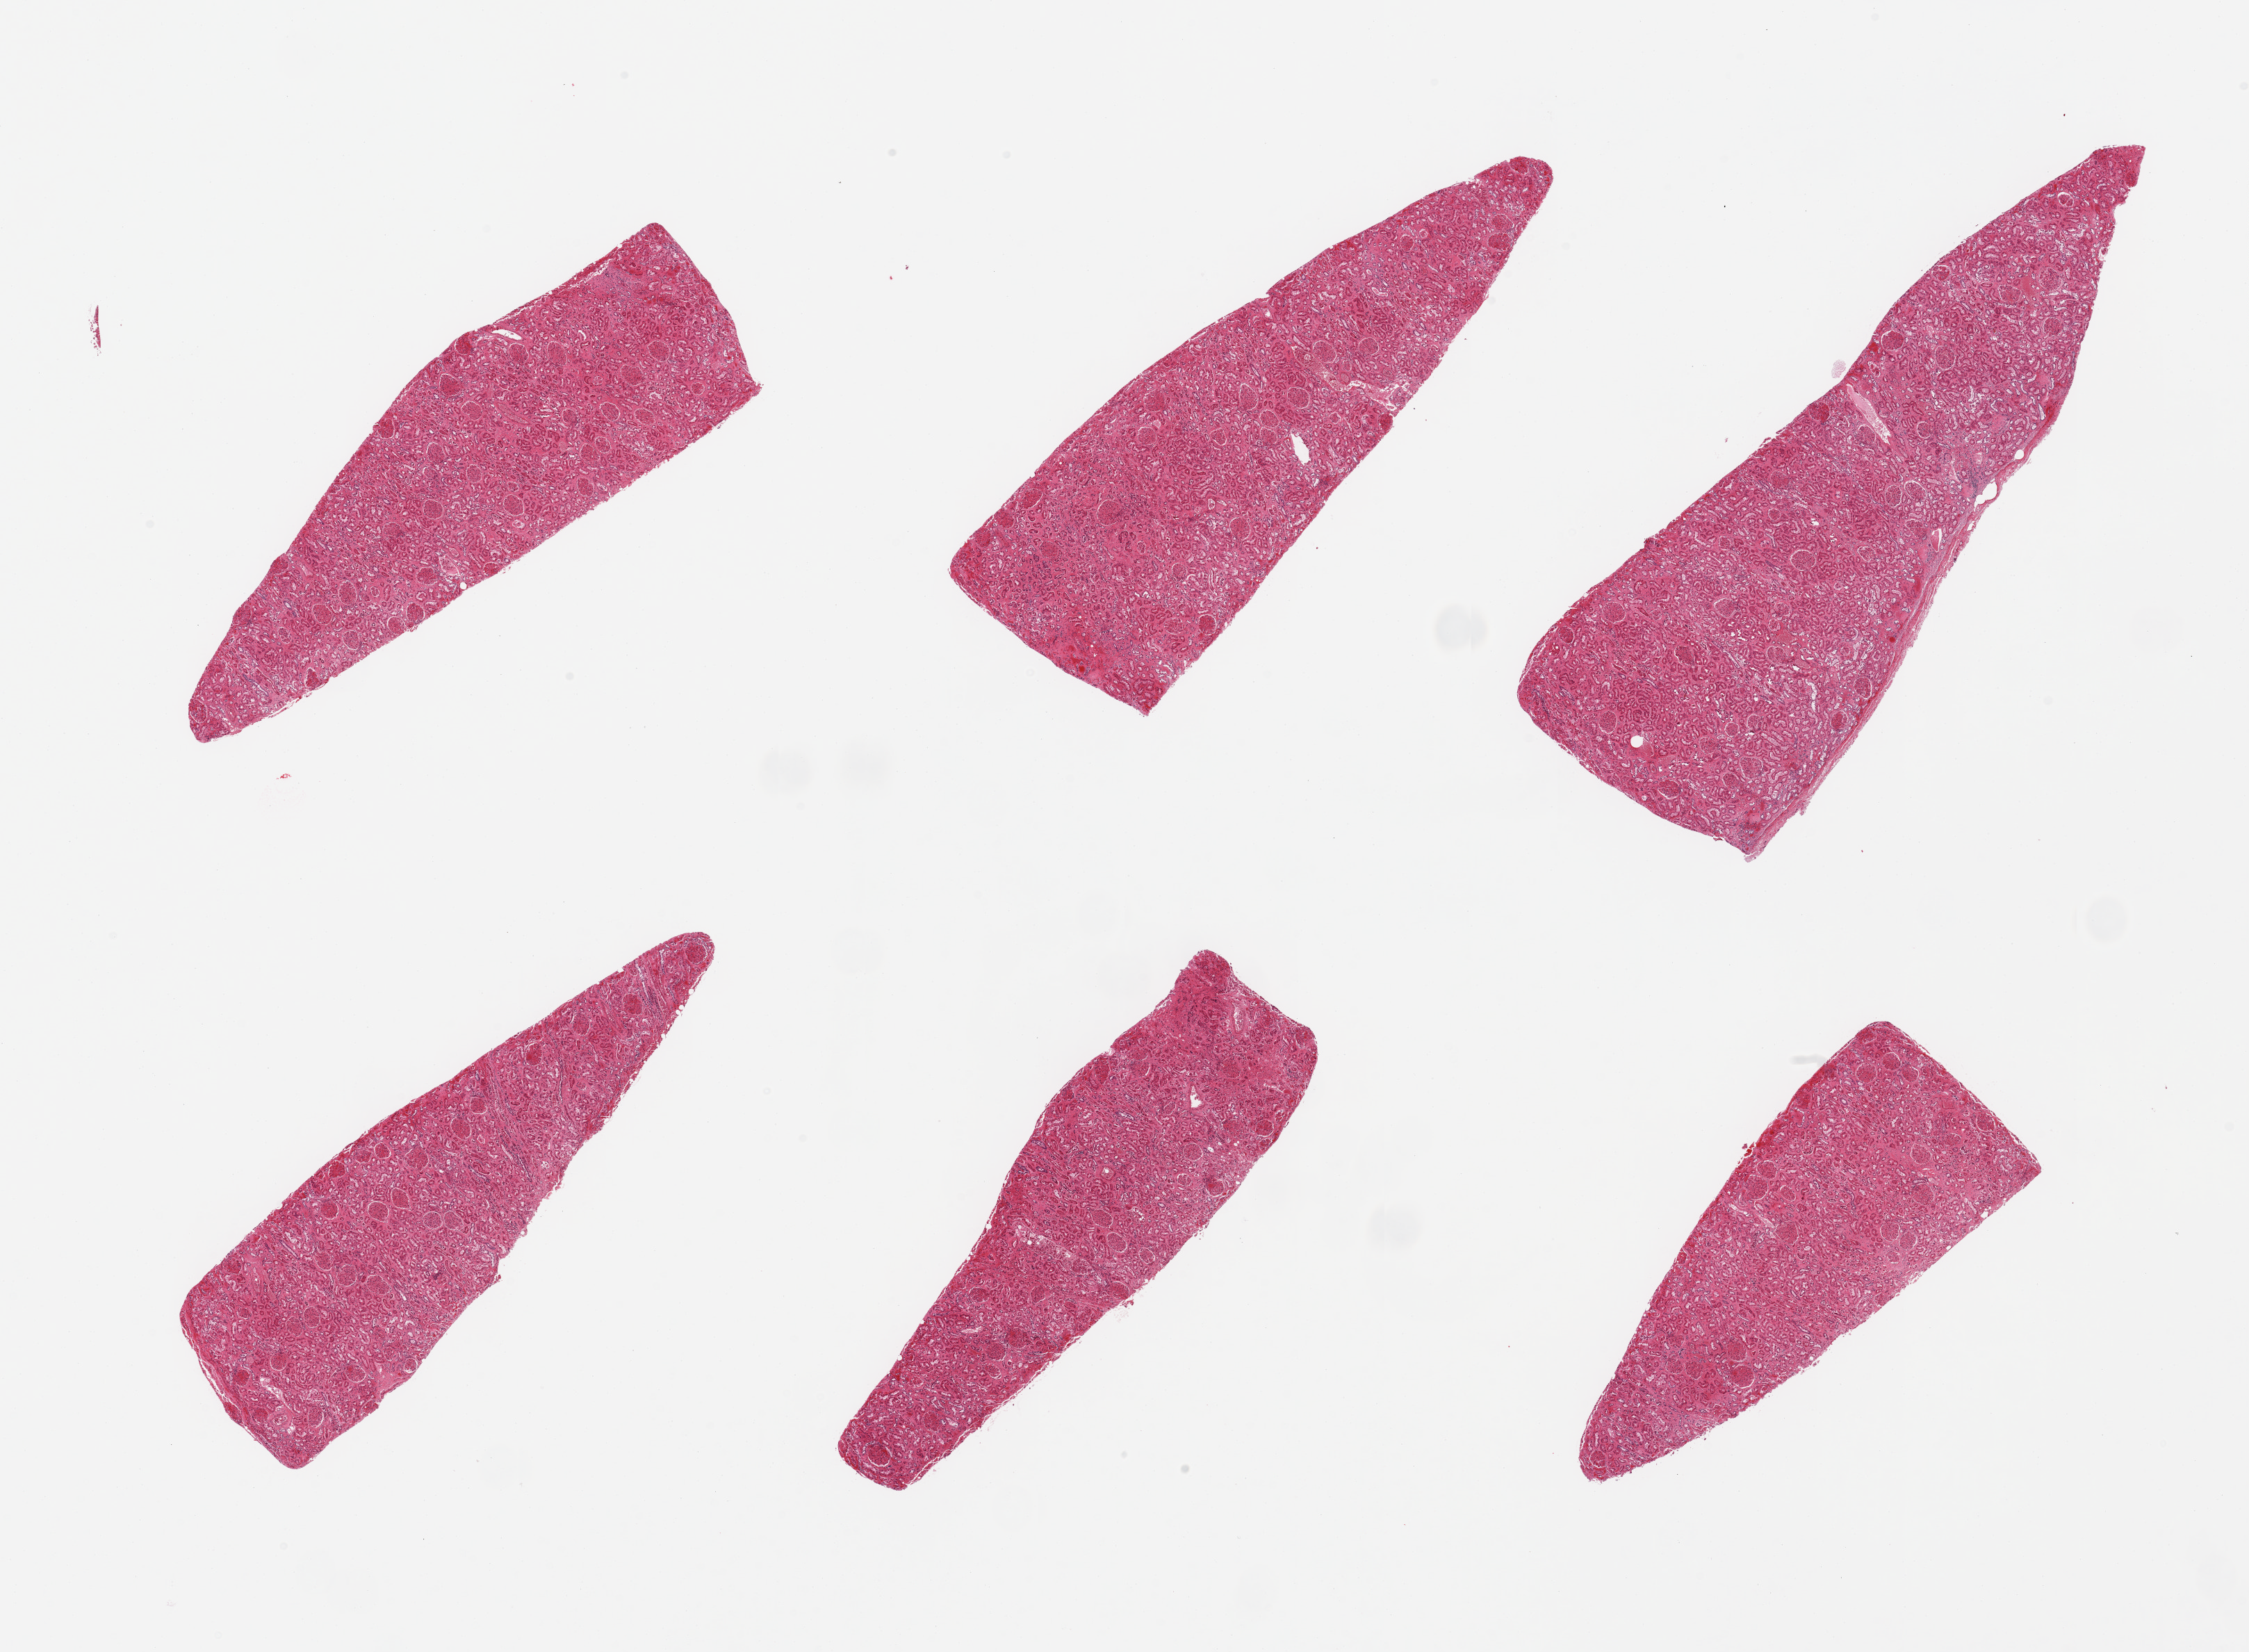
Digitized hematoxylin and eosin (H&E)-stained section, low-resolution overview of the scanned area, about 25.6 x 18.8 mm; PAXgene-fixed, paraffin-embedded tissue; sampled site (target tissue): renal cortex; tissue donor sample. Donor sex: male.
Pathologist's review note for this sample: 6 pieces; no active or chronic lesions.